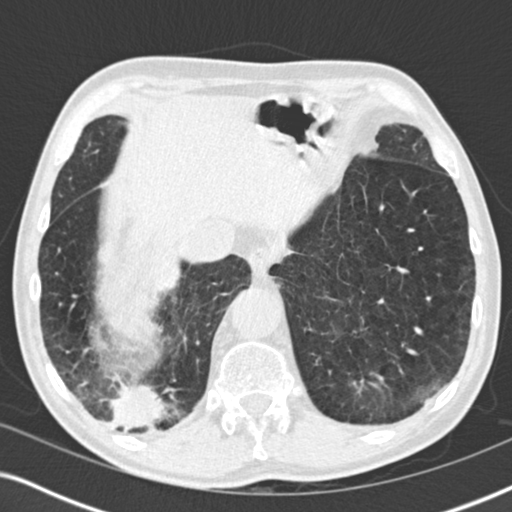
Chest CT (low-dose screening protocol), one axial image; first (baseline) screen; lung window (W 1500 / L -600 HU); slice 145 of 196 in the series. Male participant, aged 64 years at enrolment. Former smoker at enrolment.
Expert reader's lesion annotation, bounding box (x1, y1, x2, y2) in pixels: (76, 363, 180, 451). The screening reader recorded 3 non-calcified nodules or masses ≥4 mm on this exam (lingula, lingula, right lower lobe); which of them this box marks is not recorded. Lung cancer was diagnosed 27 days after this screen: squamous cell carcinoma, NOS, right lower lobe, moderately differentiated (G2), stage IV (AJCC 6th edition), 40 mm at pathology.